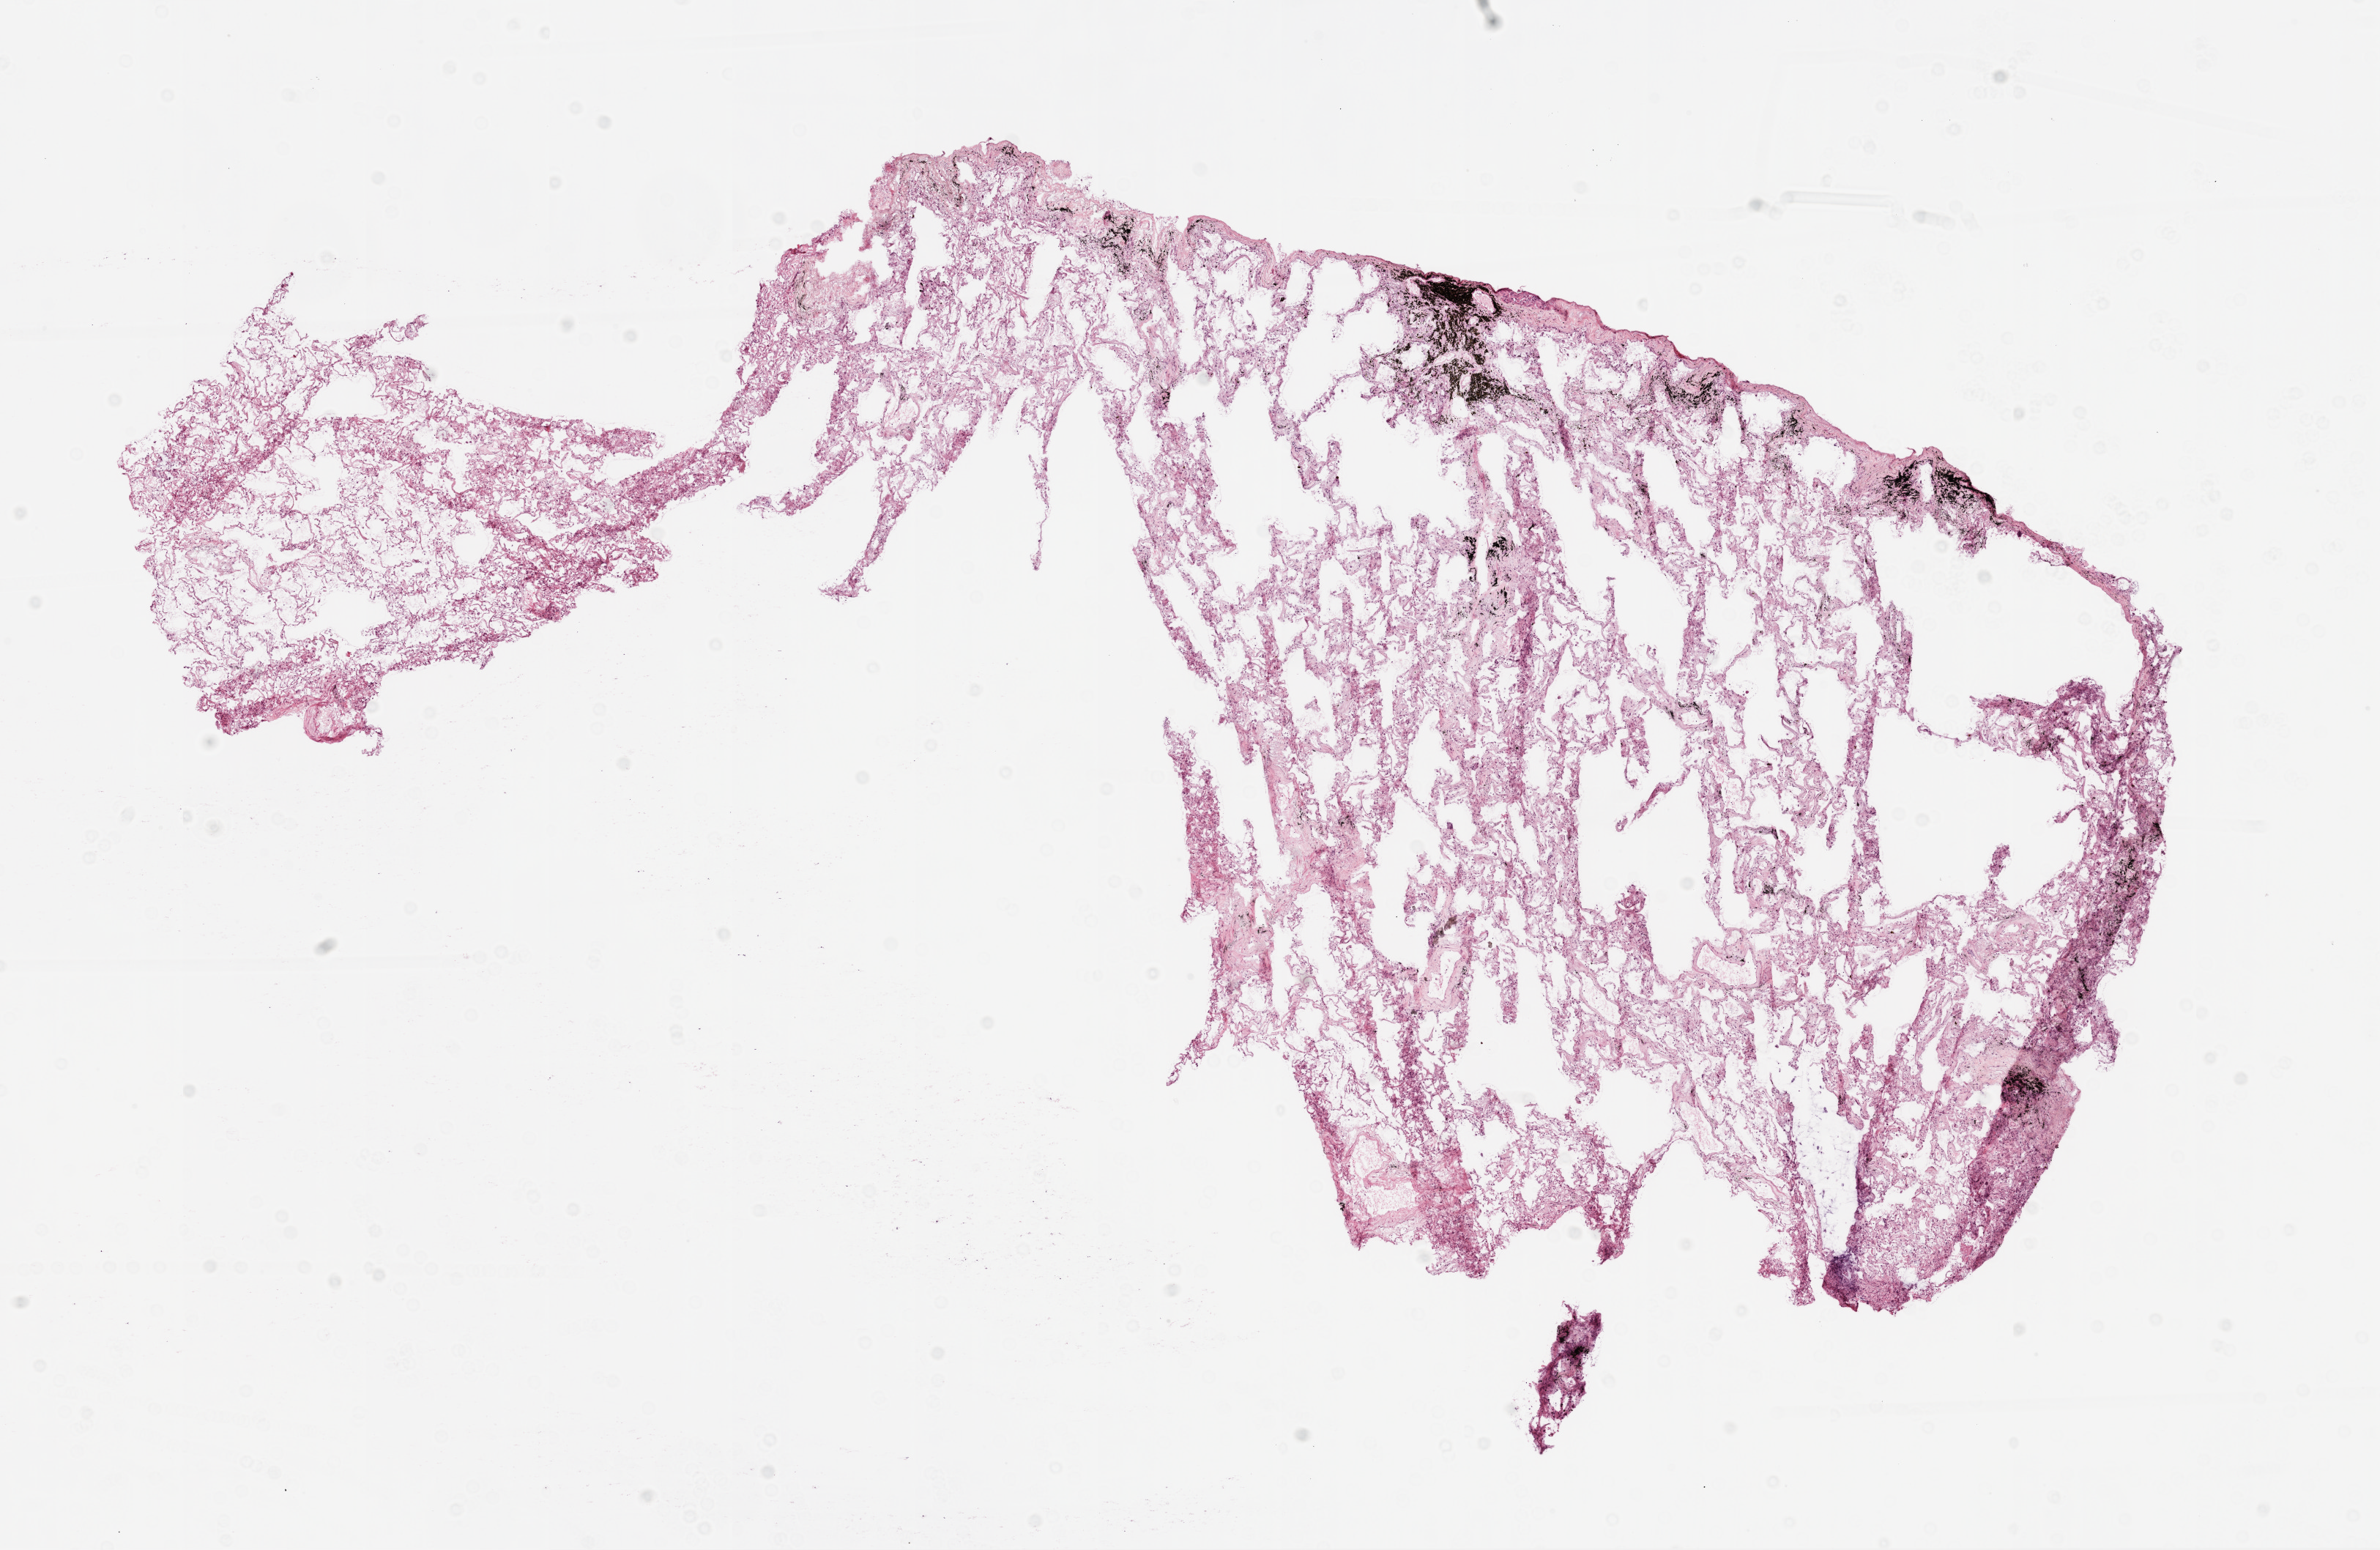
H&E-stained whole-slide image — whole scanned area (about 13.0 x 8.5 mm) shown as a low-resolution overview. Frozen section from the top of the tissue portion. Lung, solid tissue normal (non-tumour tissue) sample. Male, age 74 years at initial diagnosis.
- this section: solid tissue normal (non-tumour) sample from the same patient
- patient diagnosis: Squamous cell carcinoma, NOS (upper lobe, lung)